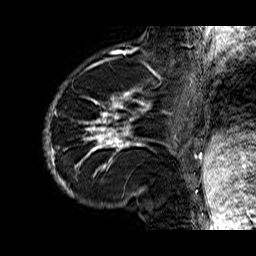
Breast MRI (dynamic contrast-enhanced), one sagittal slice; dynamic contrast-enhanced series, time point 2 of 6 at this slice position (early post-contrast); 1.5 T; TE 6.3 ms, TR 32.9 ms; 4 mm slice thickness; 256 × 256 image matrix, field of view 200 × 200 mm. Female patient. From the clinical record (not read from this slice): setting: breast cancer imaged before/during neoadjuvant chemotherapy; receptor status: HR-positive, HER2-negative.
Annotated regions visible in this slice (semi-automatically segmented with operator editing):
- analysis volume of interest (the breast-tissue region the enhancement analysis was run in; not a lesion): bounding box [x1, y1, x2, y2] px = [44, 74, 176, 210]
- tumour enhancement mask (voxels above the 100 % enhancement threshold inside the analysis volume of interest): [44, 82, 176, 196]